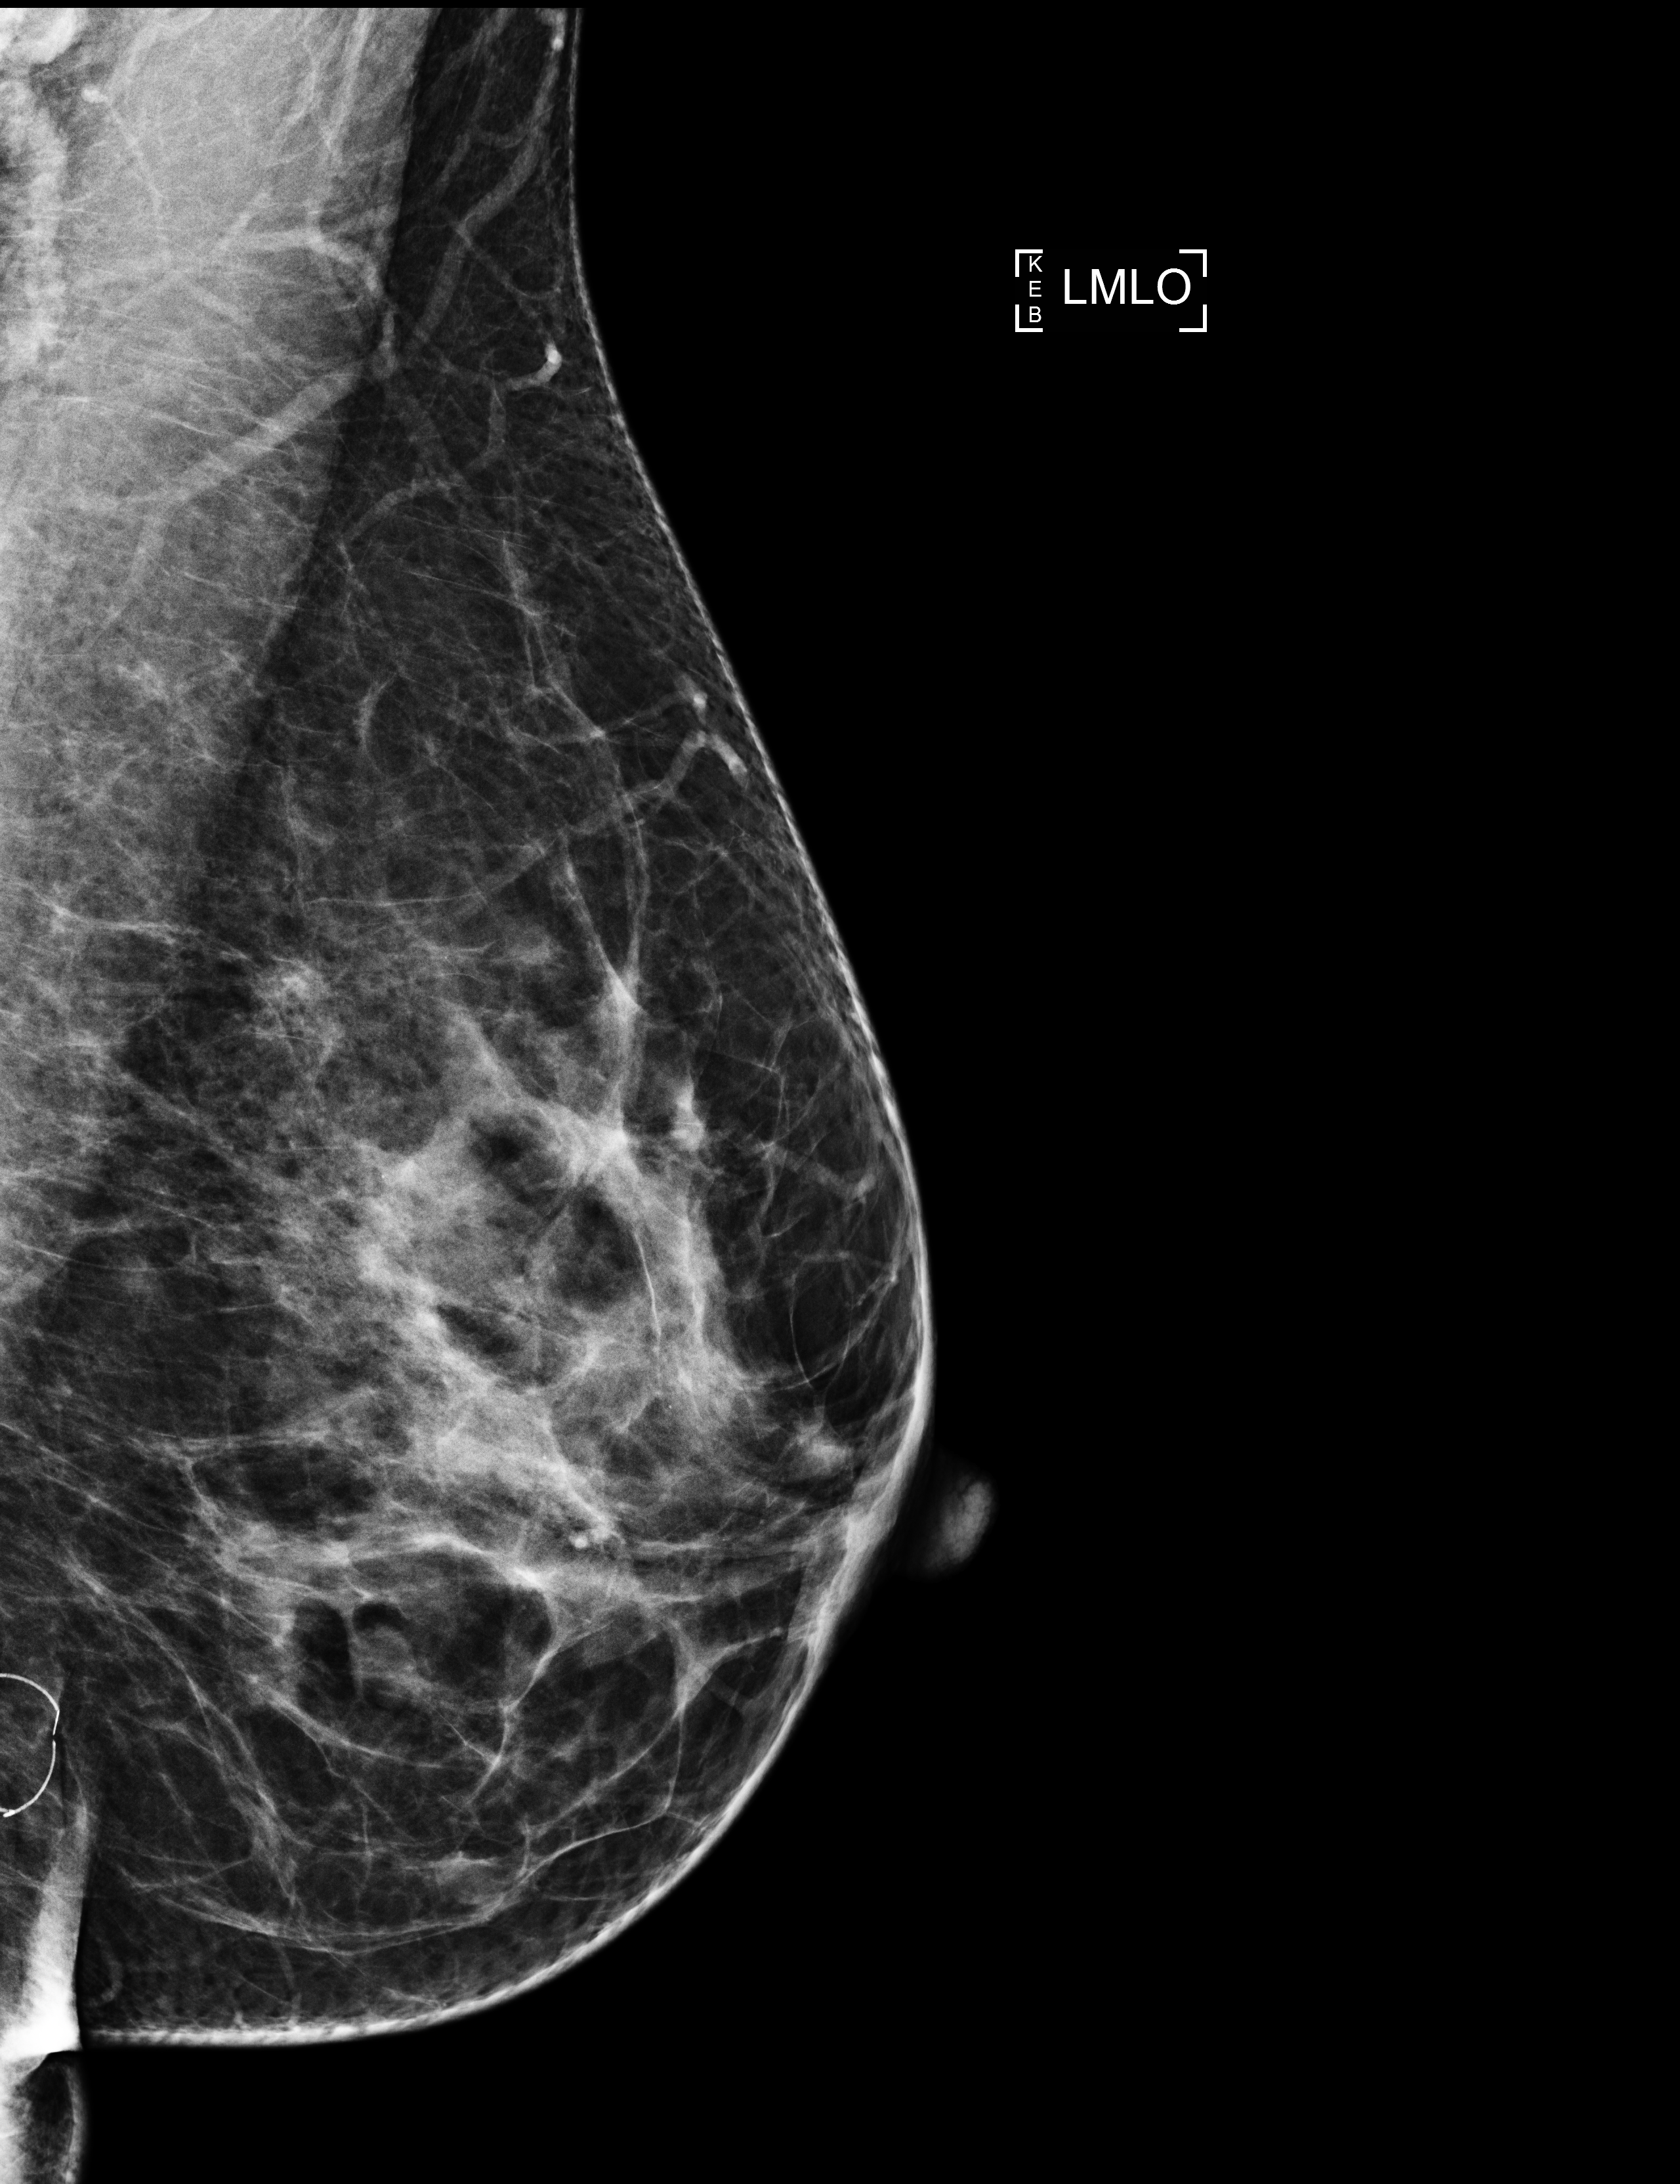
Full-field digital mammogram (FFDM); left breast; mediolateral oblique (MLO) view; annual screening mammography examination; compressed breast thickness 64 mm. Patient aged 41 years (female).
Breast density at the screening exam (both breasts): heterogeneously dense (BI-RADS density category c). Final BI-RADS assessment for this screening round (tomosynthesis exam, both breasts): category 3. Recall: recalled for additional imaging after this screen.